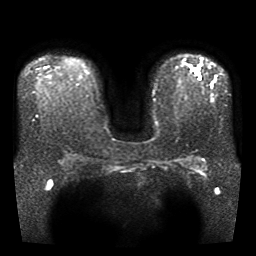
Breast MRI, one axial slice; slice 27 of 40 in the series (ordered by position); diffusion-weighted series; image 2 of 4 stored at this slice position (different b-values; order by instance number); 1.5 T; 5 mm slice thickness; 256 × 256 image matrix. Female patient.
Outlined on this slice (manually delineated by an expert):
- tumour on diffusion-weighted imaging: bounding box <194,69,197,74> (left, top, right, bottom; pixels)